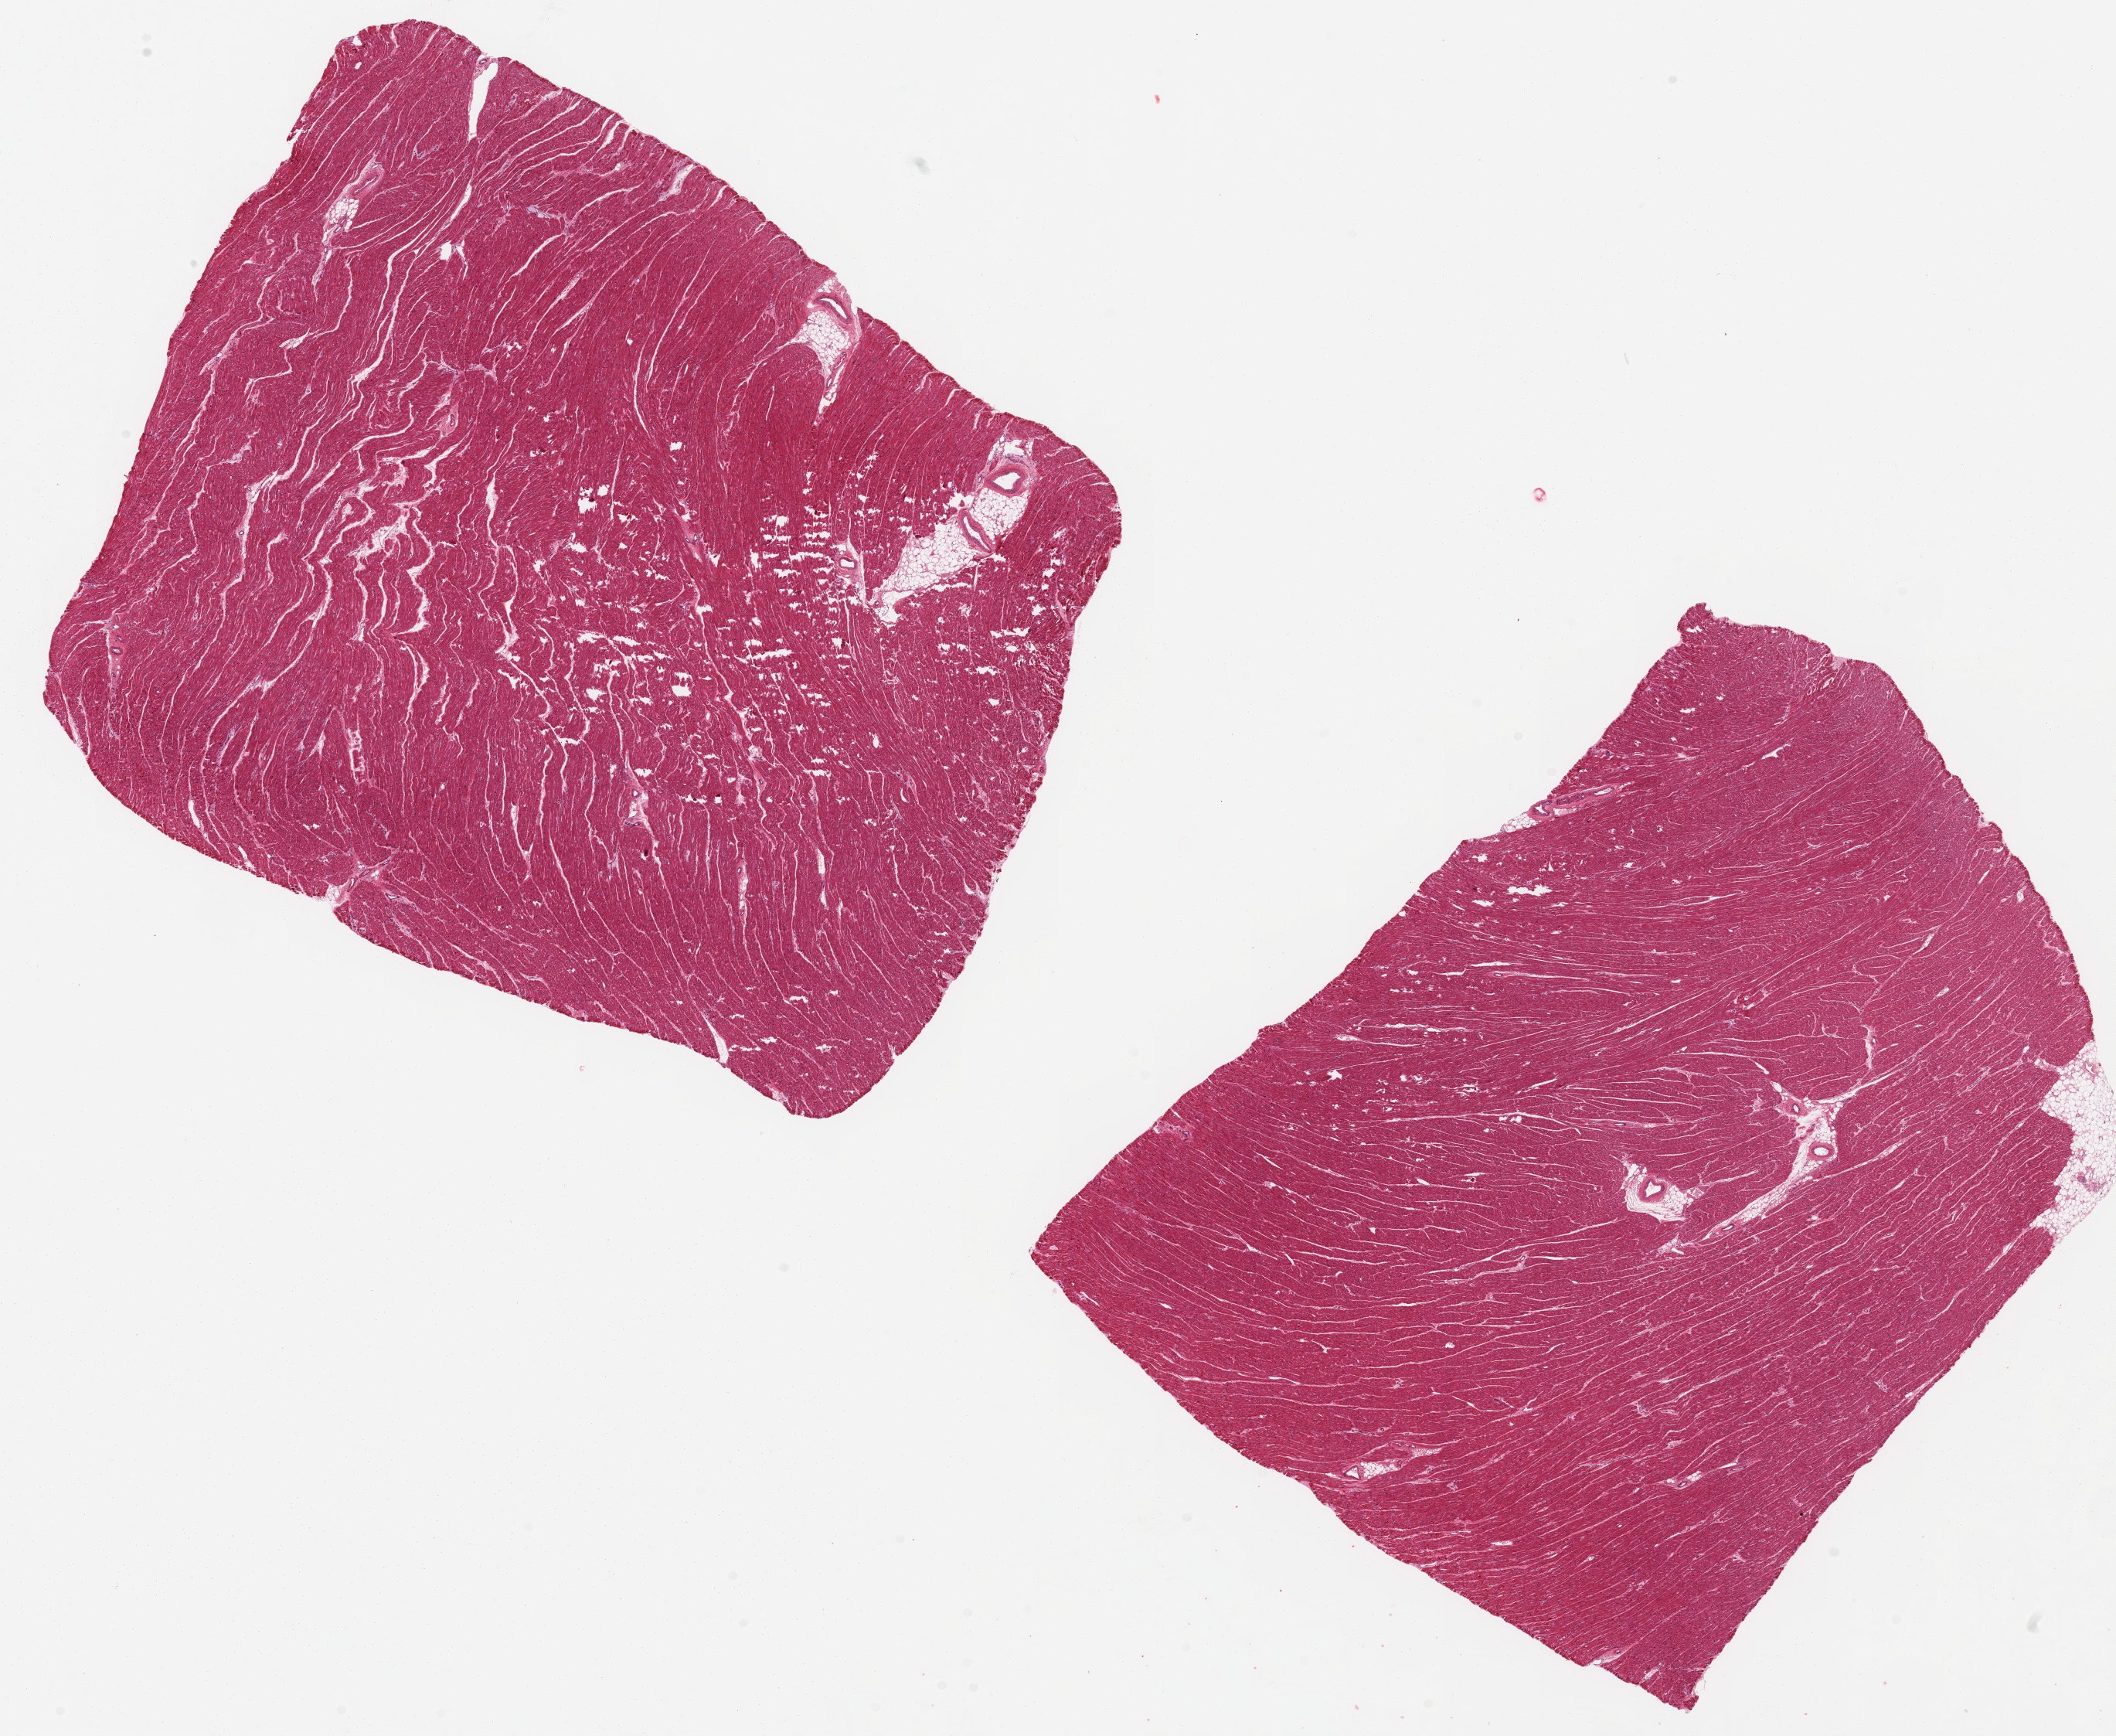
Hematoxylin and eosin (H&E) whole-slide image — a low-resolution overview of the entire scanned area, about 21.7 x 17.8 mm (slide scanned at 20x). PAXgene-fixed, paraffin-embedded tissue. Section of heart (target tissue). Tissue donor sample. Female donor.
* review note (as recorded): 2 pieces, ~10x8 mm; normal, < 5% fat